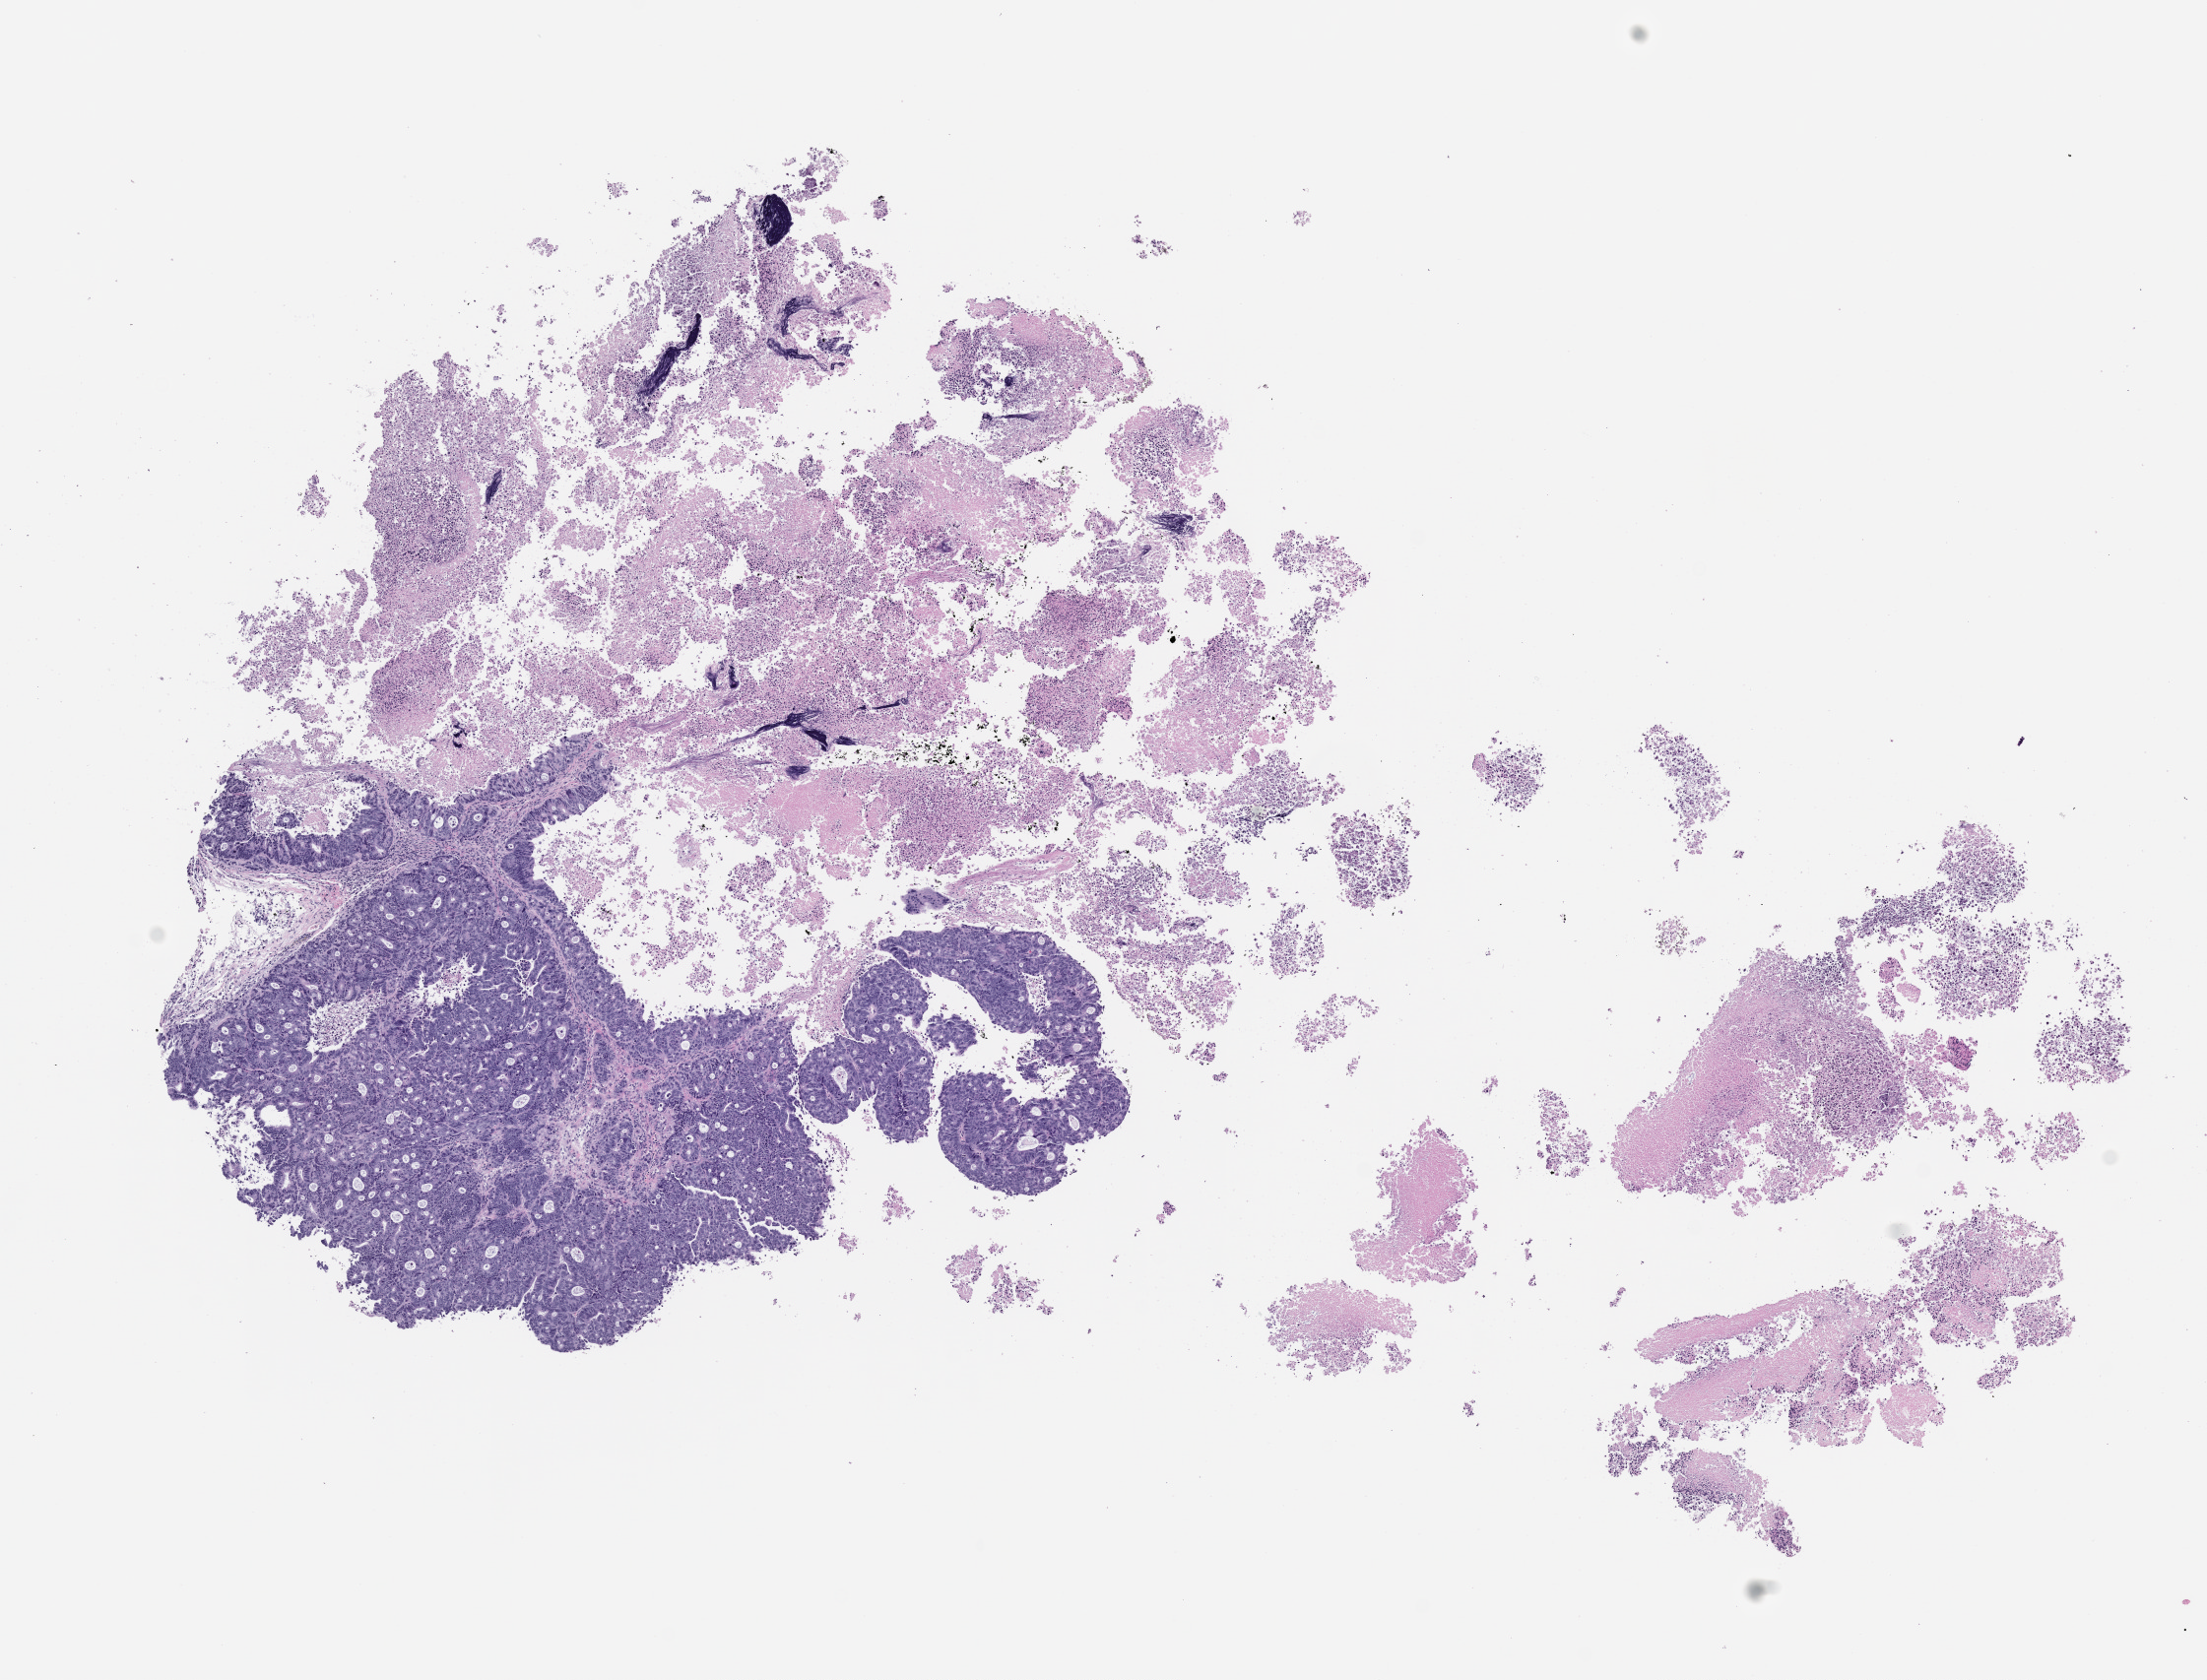
Haematoxylin and eosin whole-slide image of a patient-derived xenograft (PDX) tumor grown in a mouse, passage 2, shown as a low-resolution overview of the whole scanned area (about 9.0 x 6.9 mm); formalin-fixed paraffin-embedded section; originating tumor site category: colon.
- originating patient diagnosis: Colon Adenocarcinoma